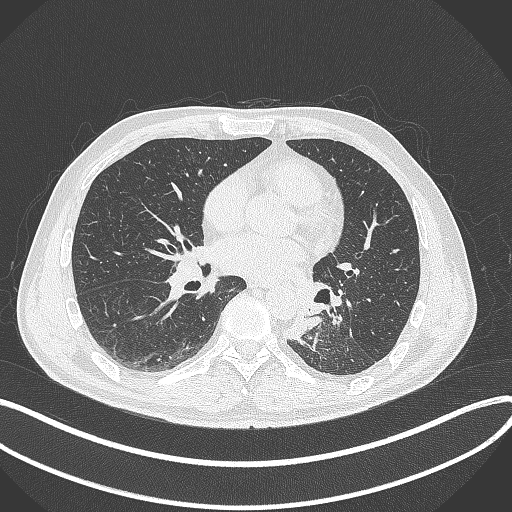
Chest CT, one axial slice. Slice 146 of 329 in the series (ordered by position). Reconstruction kernel B70f. Lung window (W 1500 / L -600 HU). 512 × 512 image matrix, field of view 400 × 400 mm. Patient: male, 59 years. From the clinical record (not read from this slice): clinical TNM (as recorded): T2a N2 M0.
Annotated regions visible in this slice (bounding box drawn by a radiologist):
- lung tumour (recorded histology: squamous cell carcinoma): box from (x=281, y=311) to (x=323, y=343) px